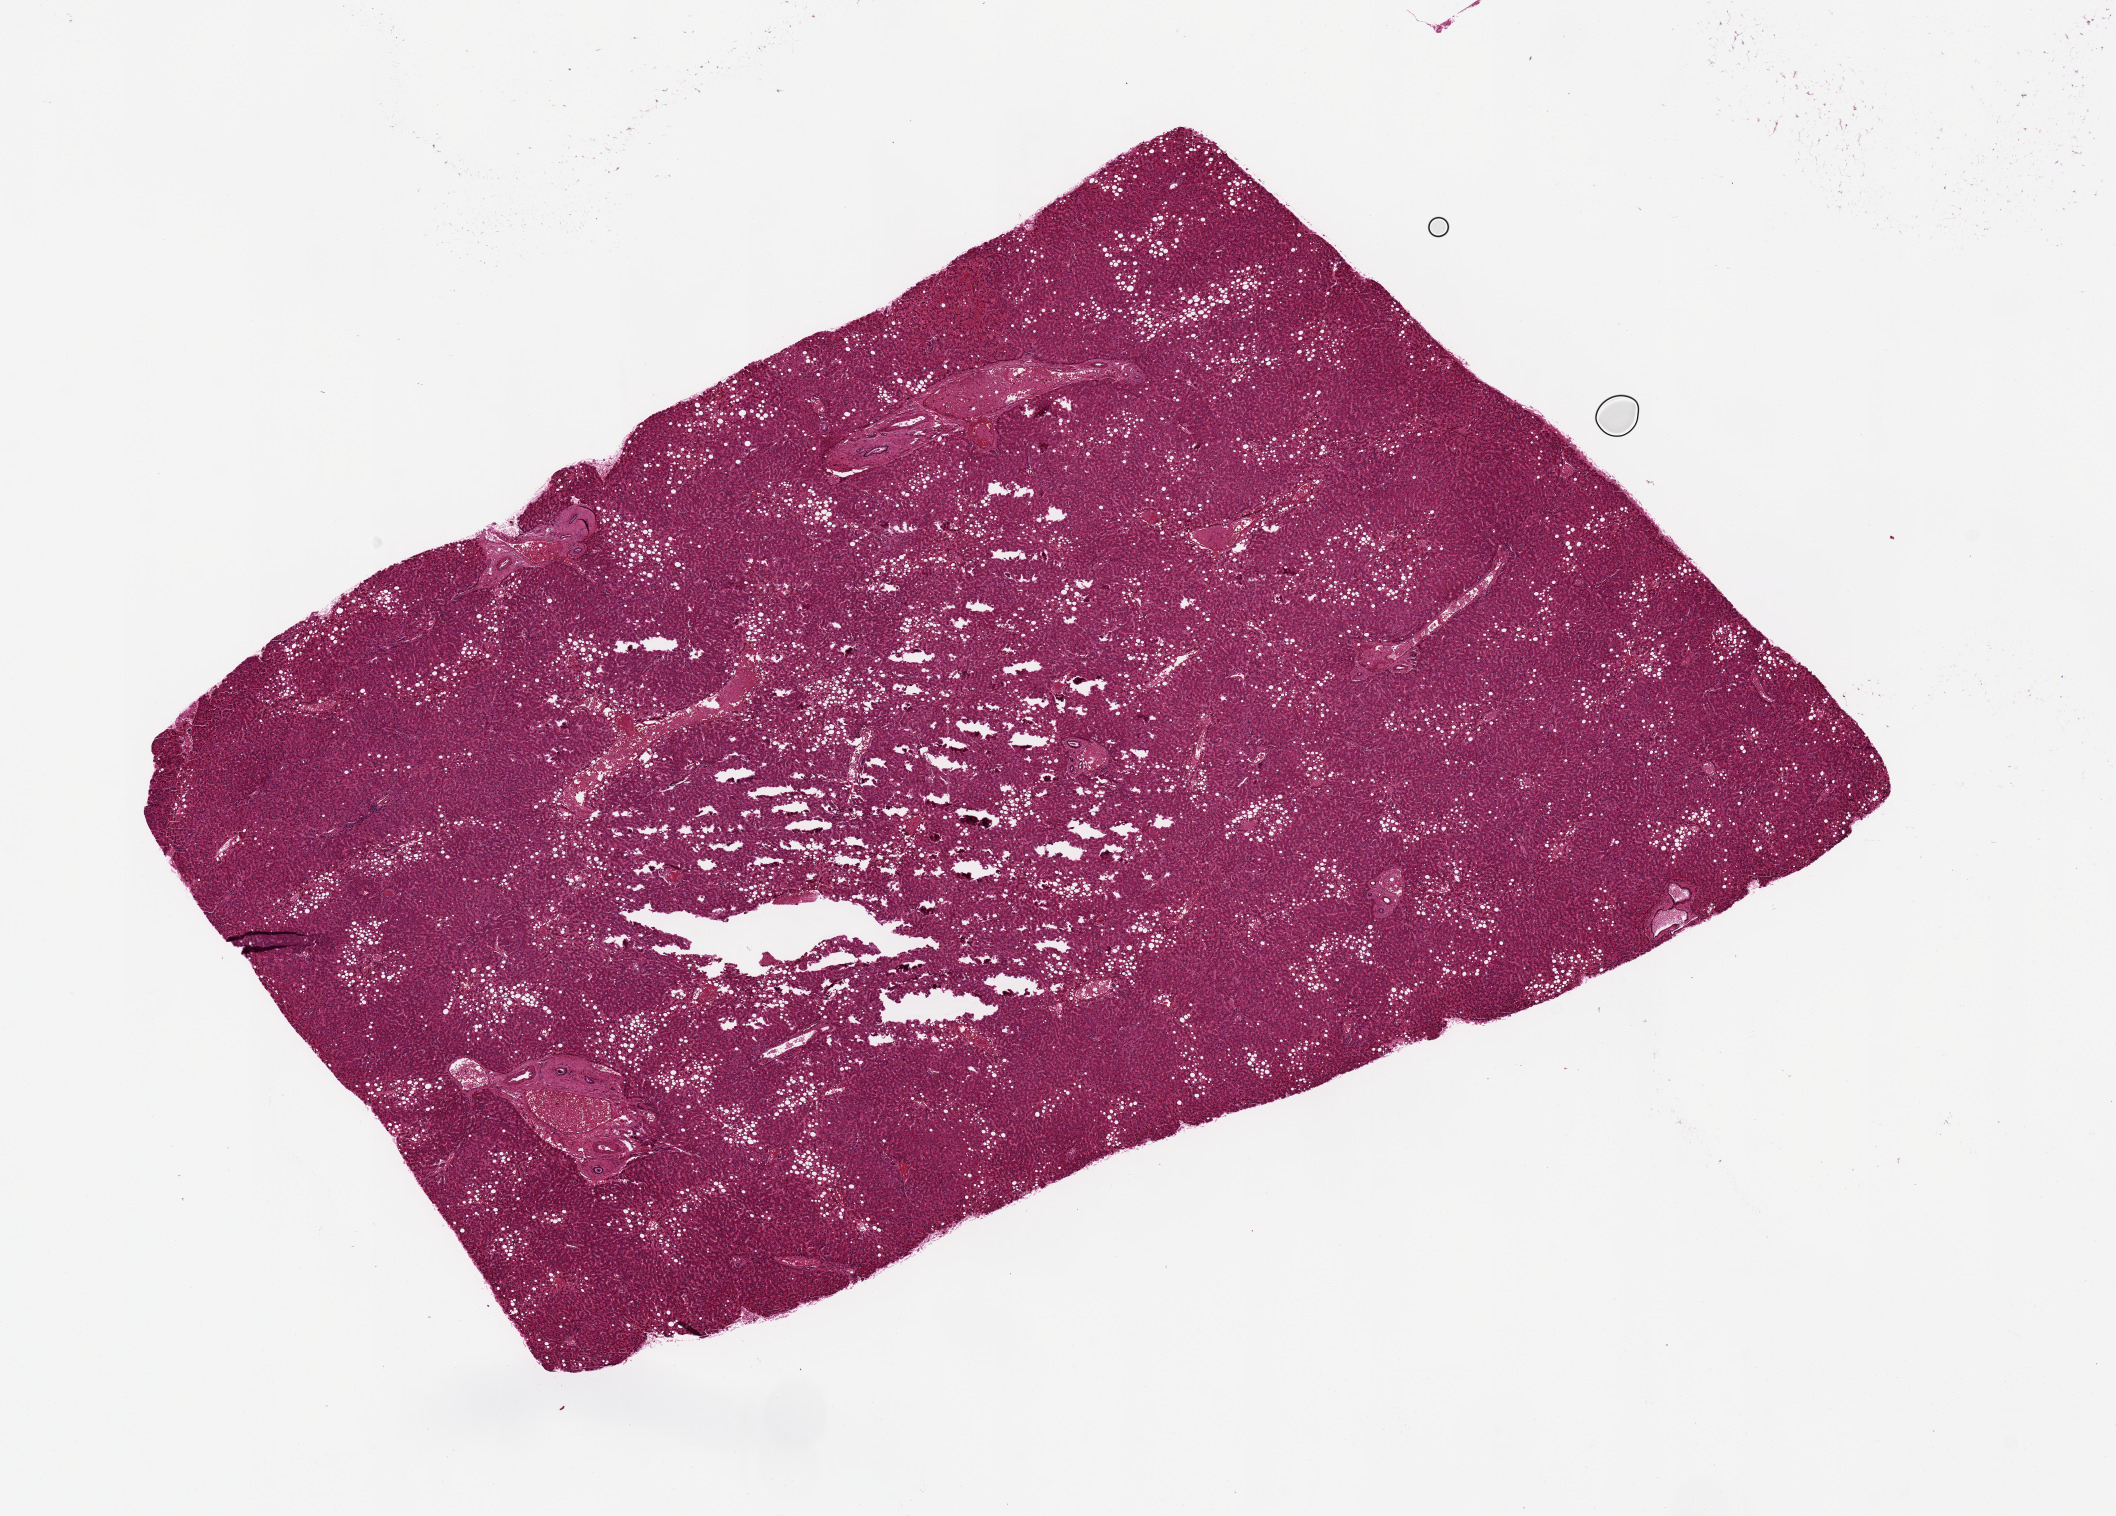
Whole-slide image, hematoxylin and eosin (H&E) stain, brightfield — whole scanned area (about 16.7 x 12.0 mm) shown as a low-resolution overview. Donor: male.
Specimen: PAXgene-fixed paraffin-embedded (PFPE) section; section of liver (target tissue); tissue donor sample.